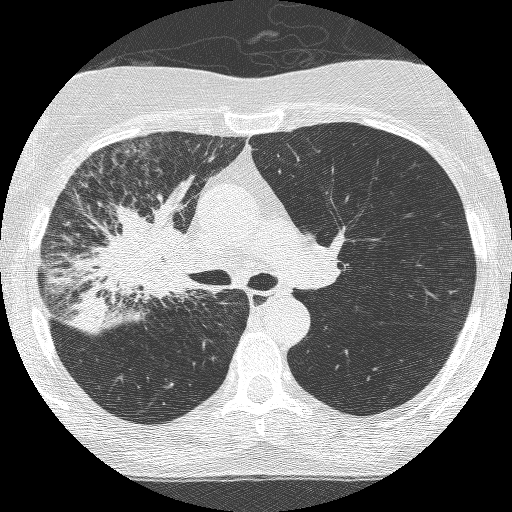
Axial slice from a low-dose chest CT screening exam, third screening round (two years after baseline), lung window (W 1500 / L -600 HU), 1.25 mm slice thickness, lung (sharp) reconstruction kernel (BONE), slice 165 of 253 in the series. Female, age 64 years at enrolment.
Expert-annotated lung lesion, bounding box [x1, y1, x2, y2] px = [82, 207, 204, 330]. Reader record for this screening exam (exam-level; its link to the box is not recorded): non-calcified nodule or mass ≥4 mm, right upper lobe, 49 × 43 mm, spiculated (stellate) margins, soft tissue attenuation, pre-existing on the prior screen: yes; interval growth: yes. Official screen result: positive, other.